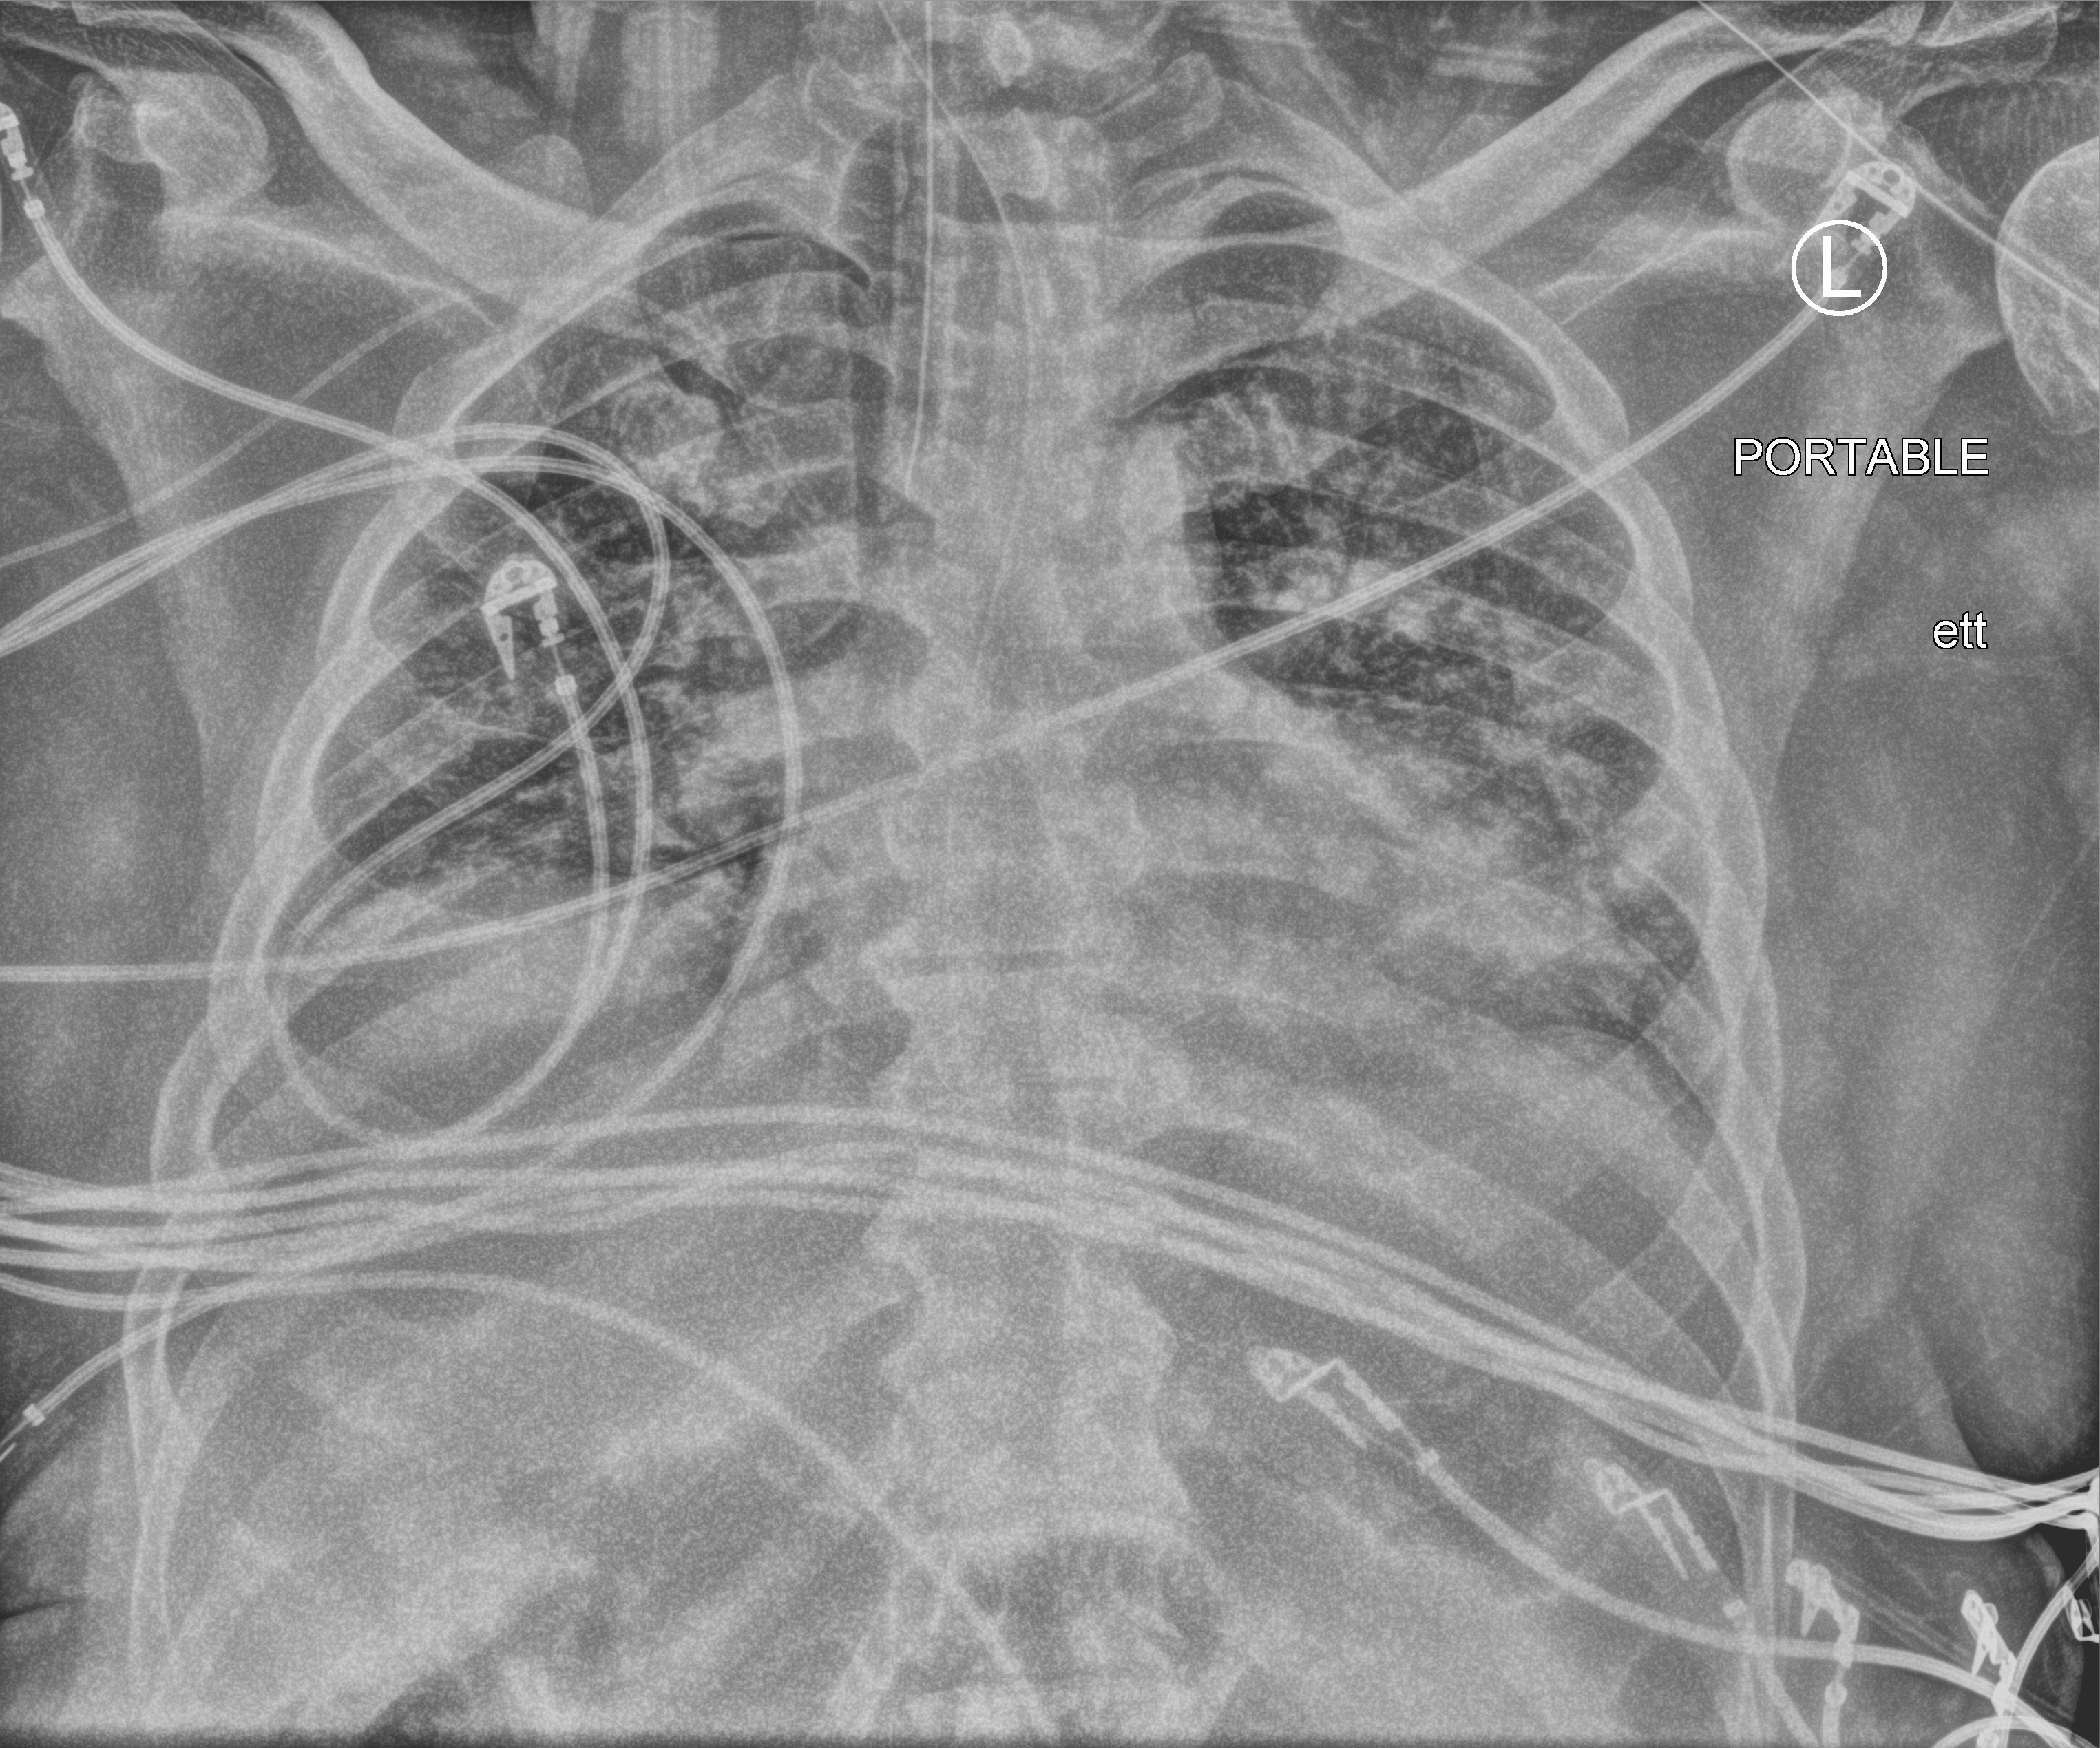
Bedside chest radiograph (computed radiography); anteroposterior (AP) projection. Patient hospitalised with COVID-19; male, aged 18–59 years.
From the hospital-stay record, not from the radiograph (when in the stay this image was taken is not recorded): length of hospital stay: 41 days; COPD (admission record): no.